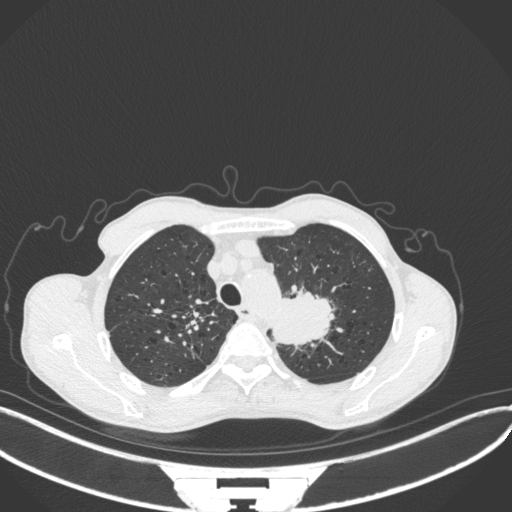
Chest CT, one axial slice; slice 338 of 394 in the series (ordered by position); reconstruction kernel B31f; lung window (W 1500 / L -600 HU); 1 mm slice thickness; 512 × 512 image matrix. Male patient, age 65 years. From the clinical record (not read from this slice): clinical TNM (as recorded): T2b N0 M0; histopathological grade: G2.
Structures marked on this image (bounding box drawn by a radiologist):
- lung tumour (recorded histology: adenocarcinoma): bounding box (x1, y1, x2, y2) in pixels: (262, 285, 337, 347)